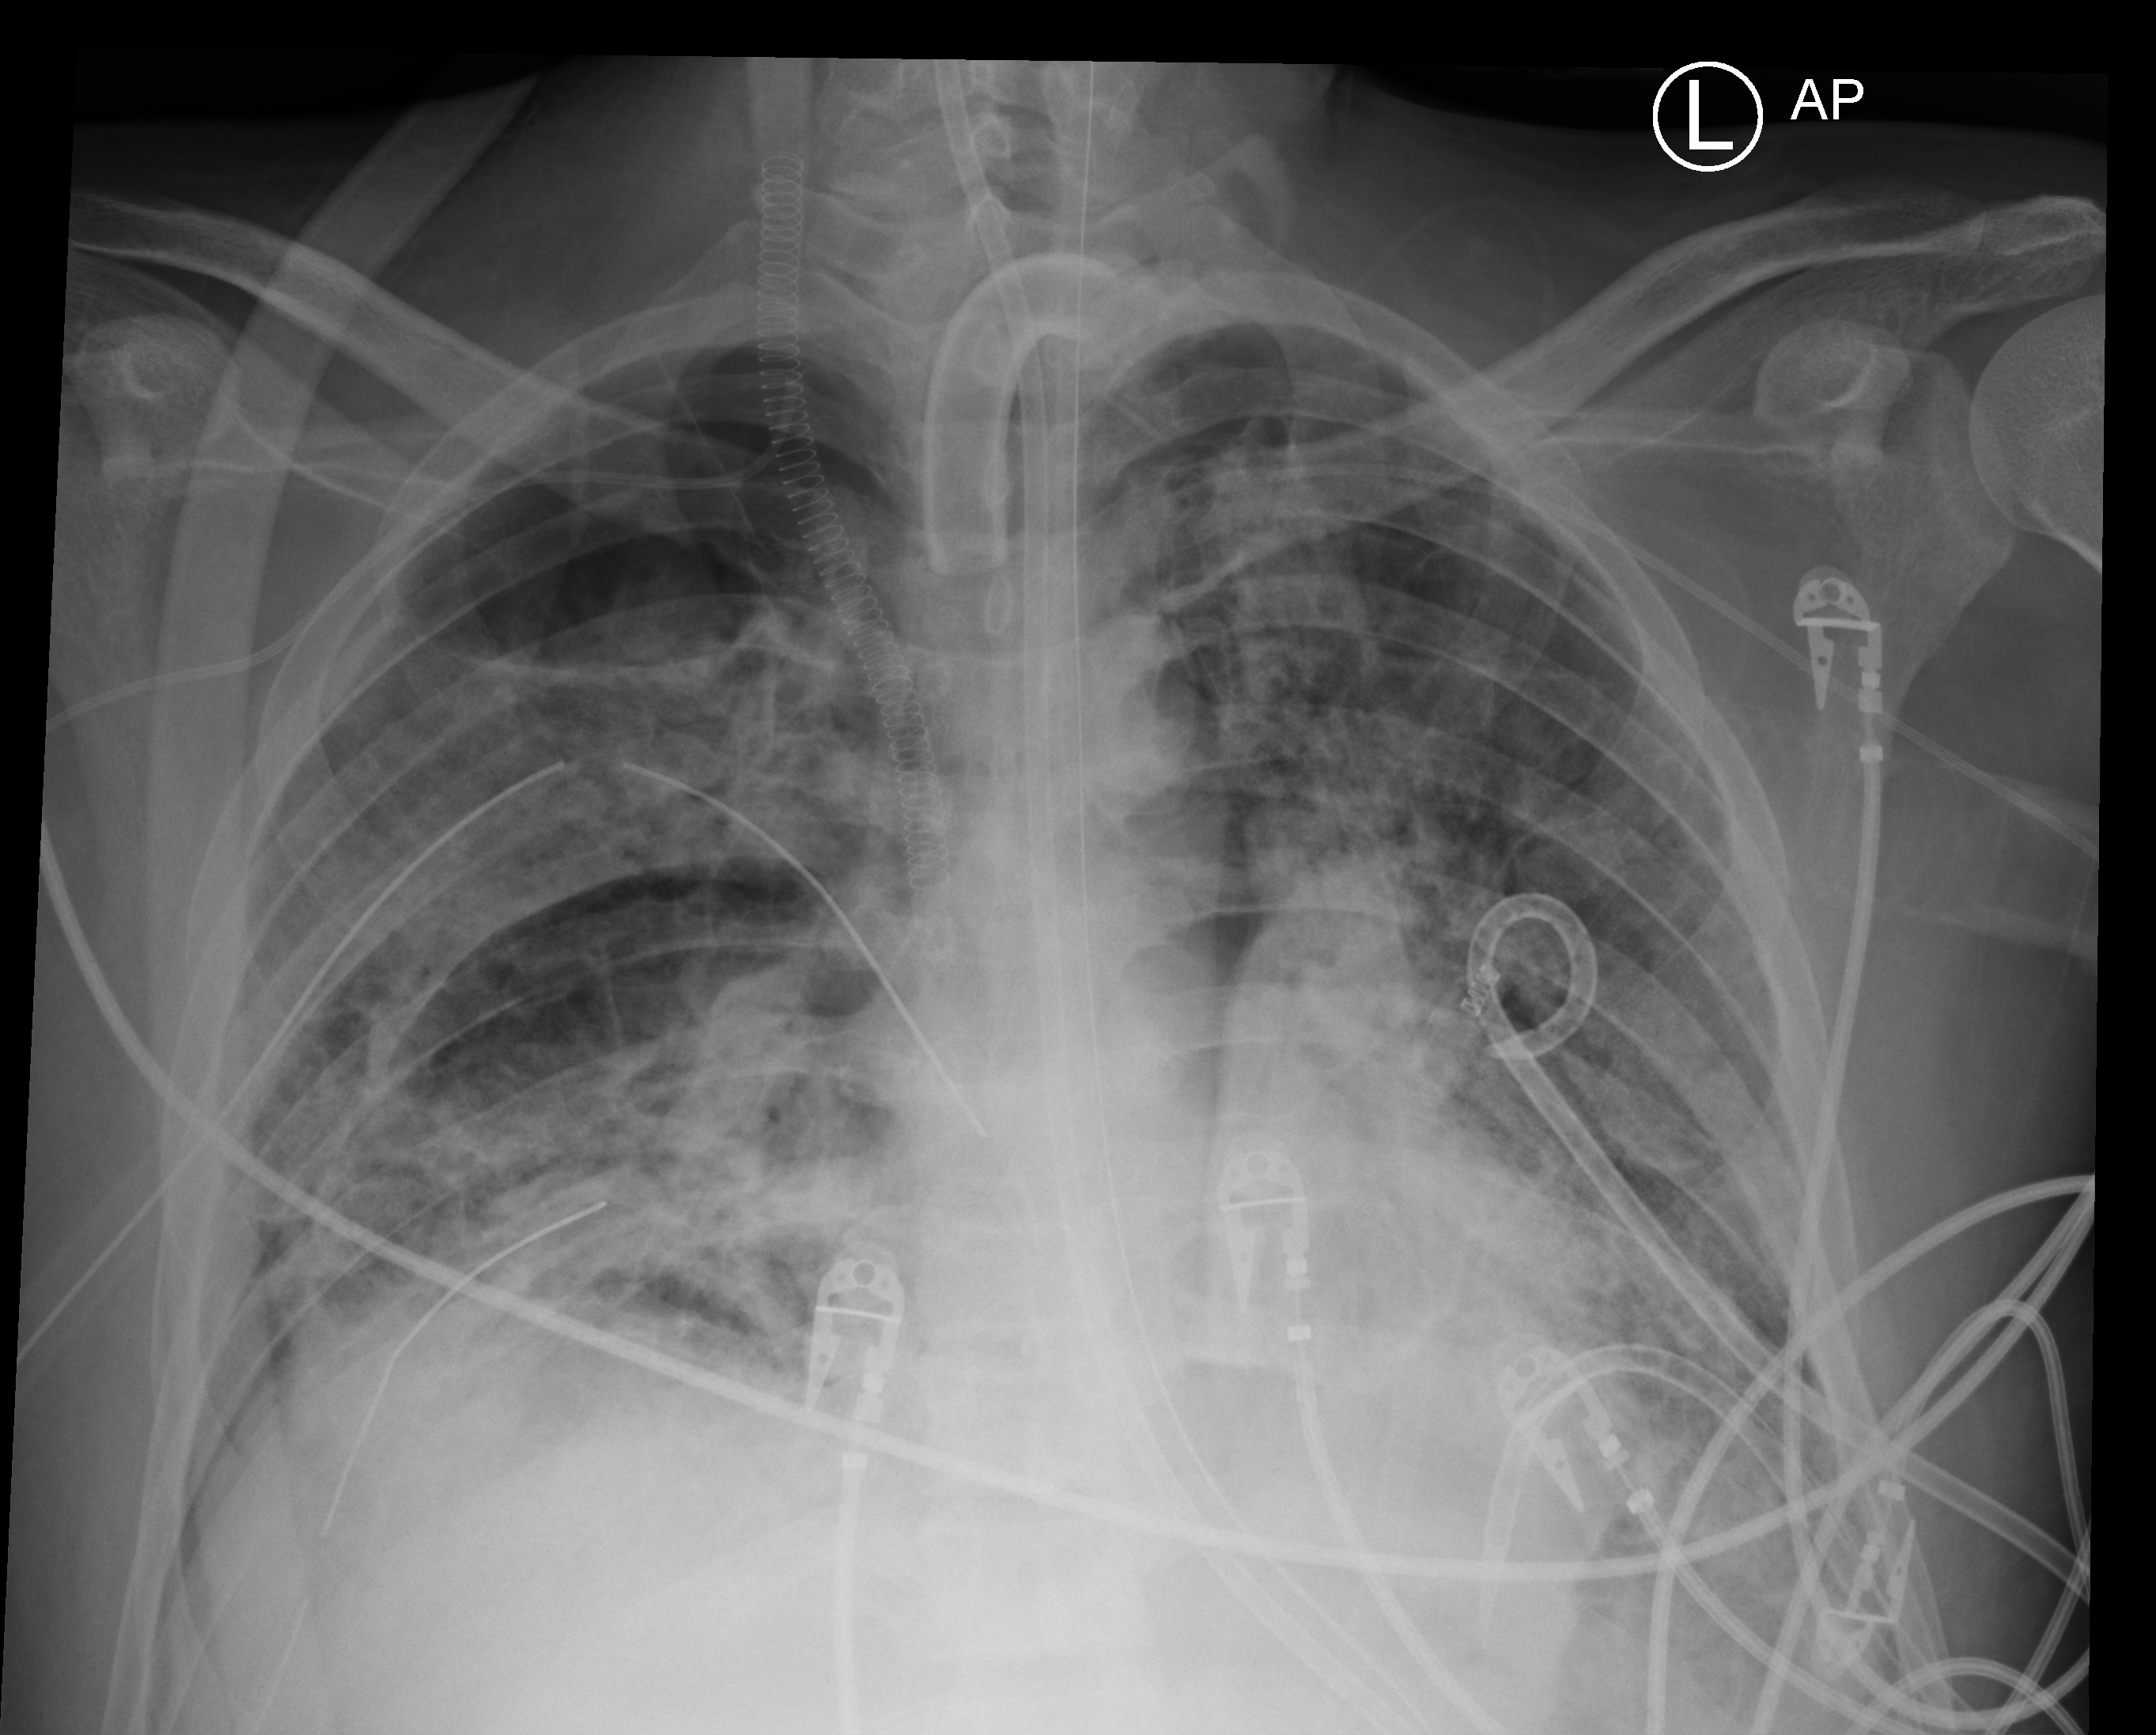
Portable chest radiograph. Patient hospitalised with COVID-19, aged 18–59 years.
Admission-level facts for this patient (not findings on this image; timing relative to this image not recorded): mechanically ventilated during this hospital stay: yes; diabetes (admission record): no.